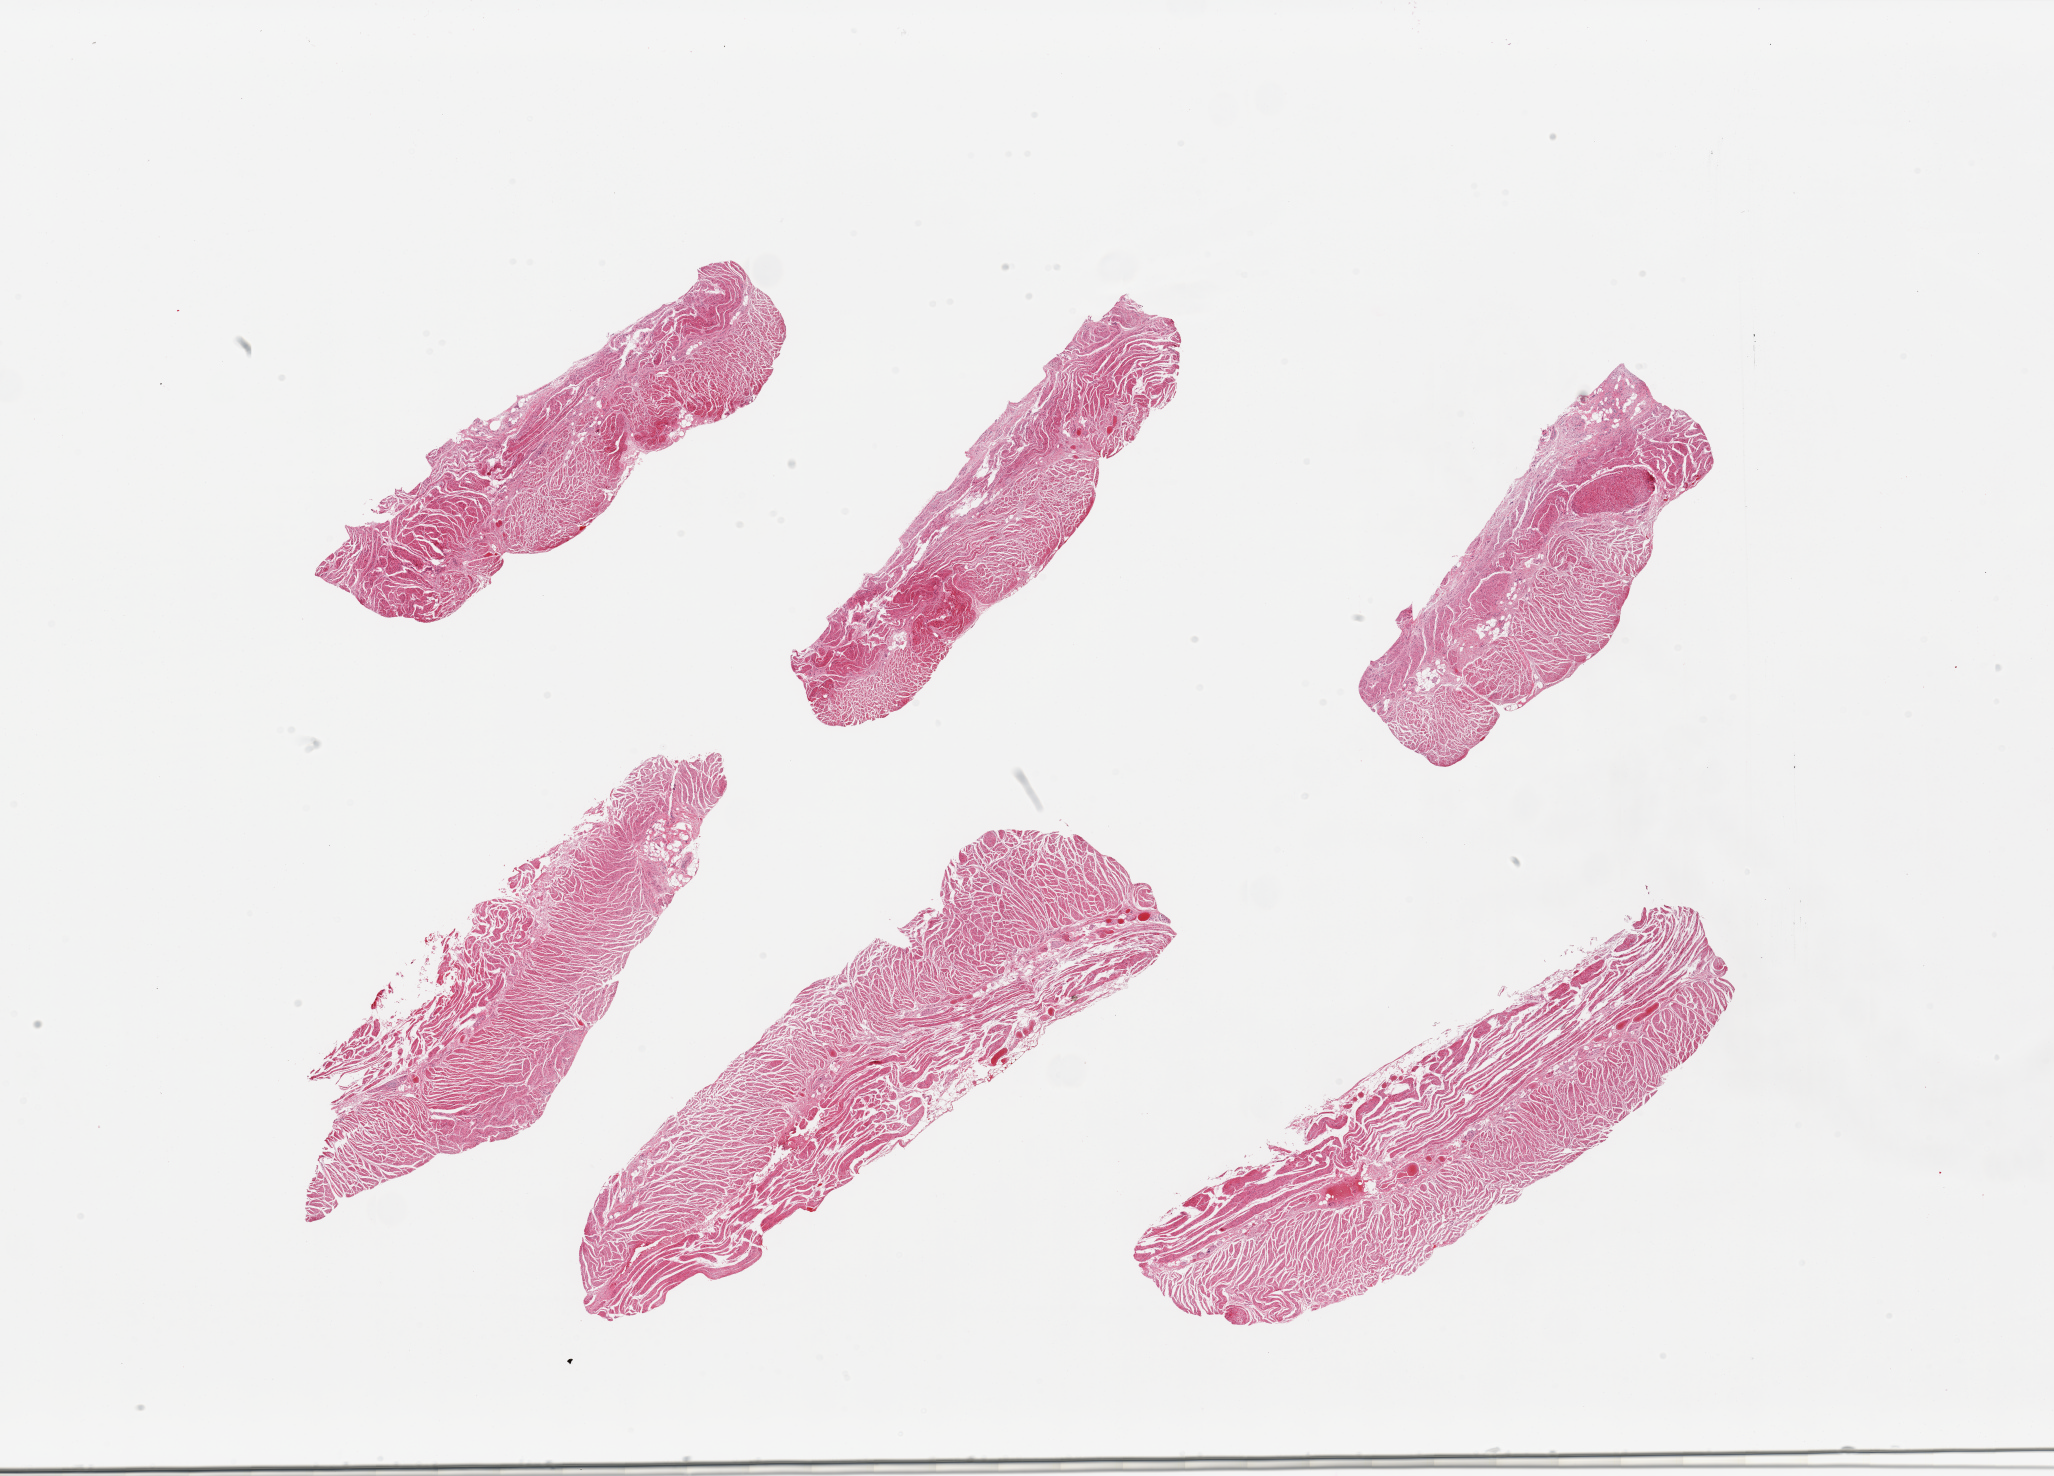
Whole-slide image, H&E stain, a low-resolution overview of the entire scanned area, about 32.5 x 23.3 mm (from a 20x scan), PAXgene-fixed, paraffin-embedded tissue, sampled site (target tissue): gastroesophageal junction, tissue donor sample.
- pathologist's review note for this sample: 6 pieces; well dissected